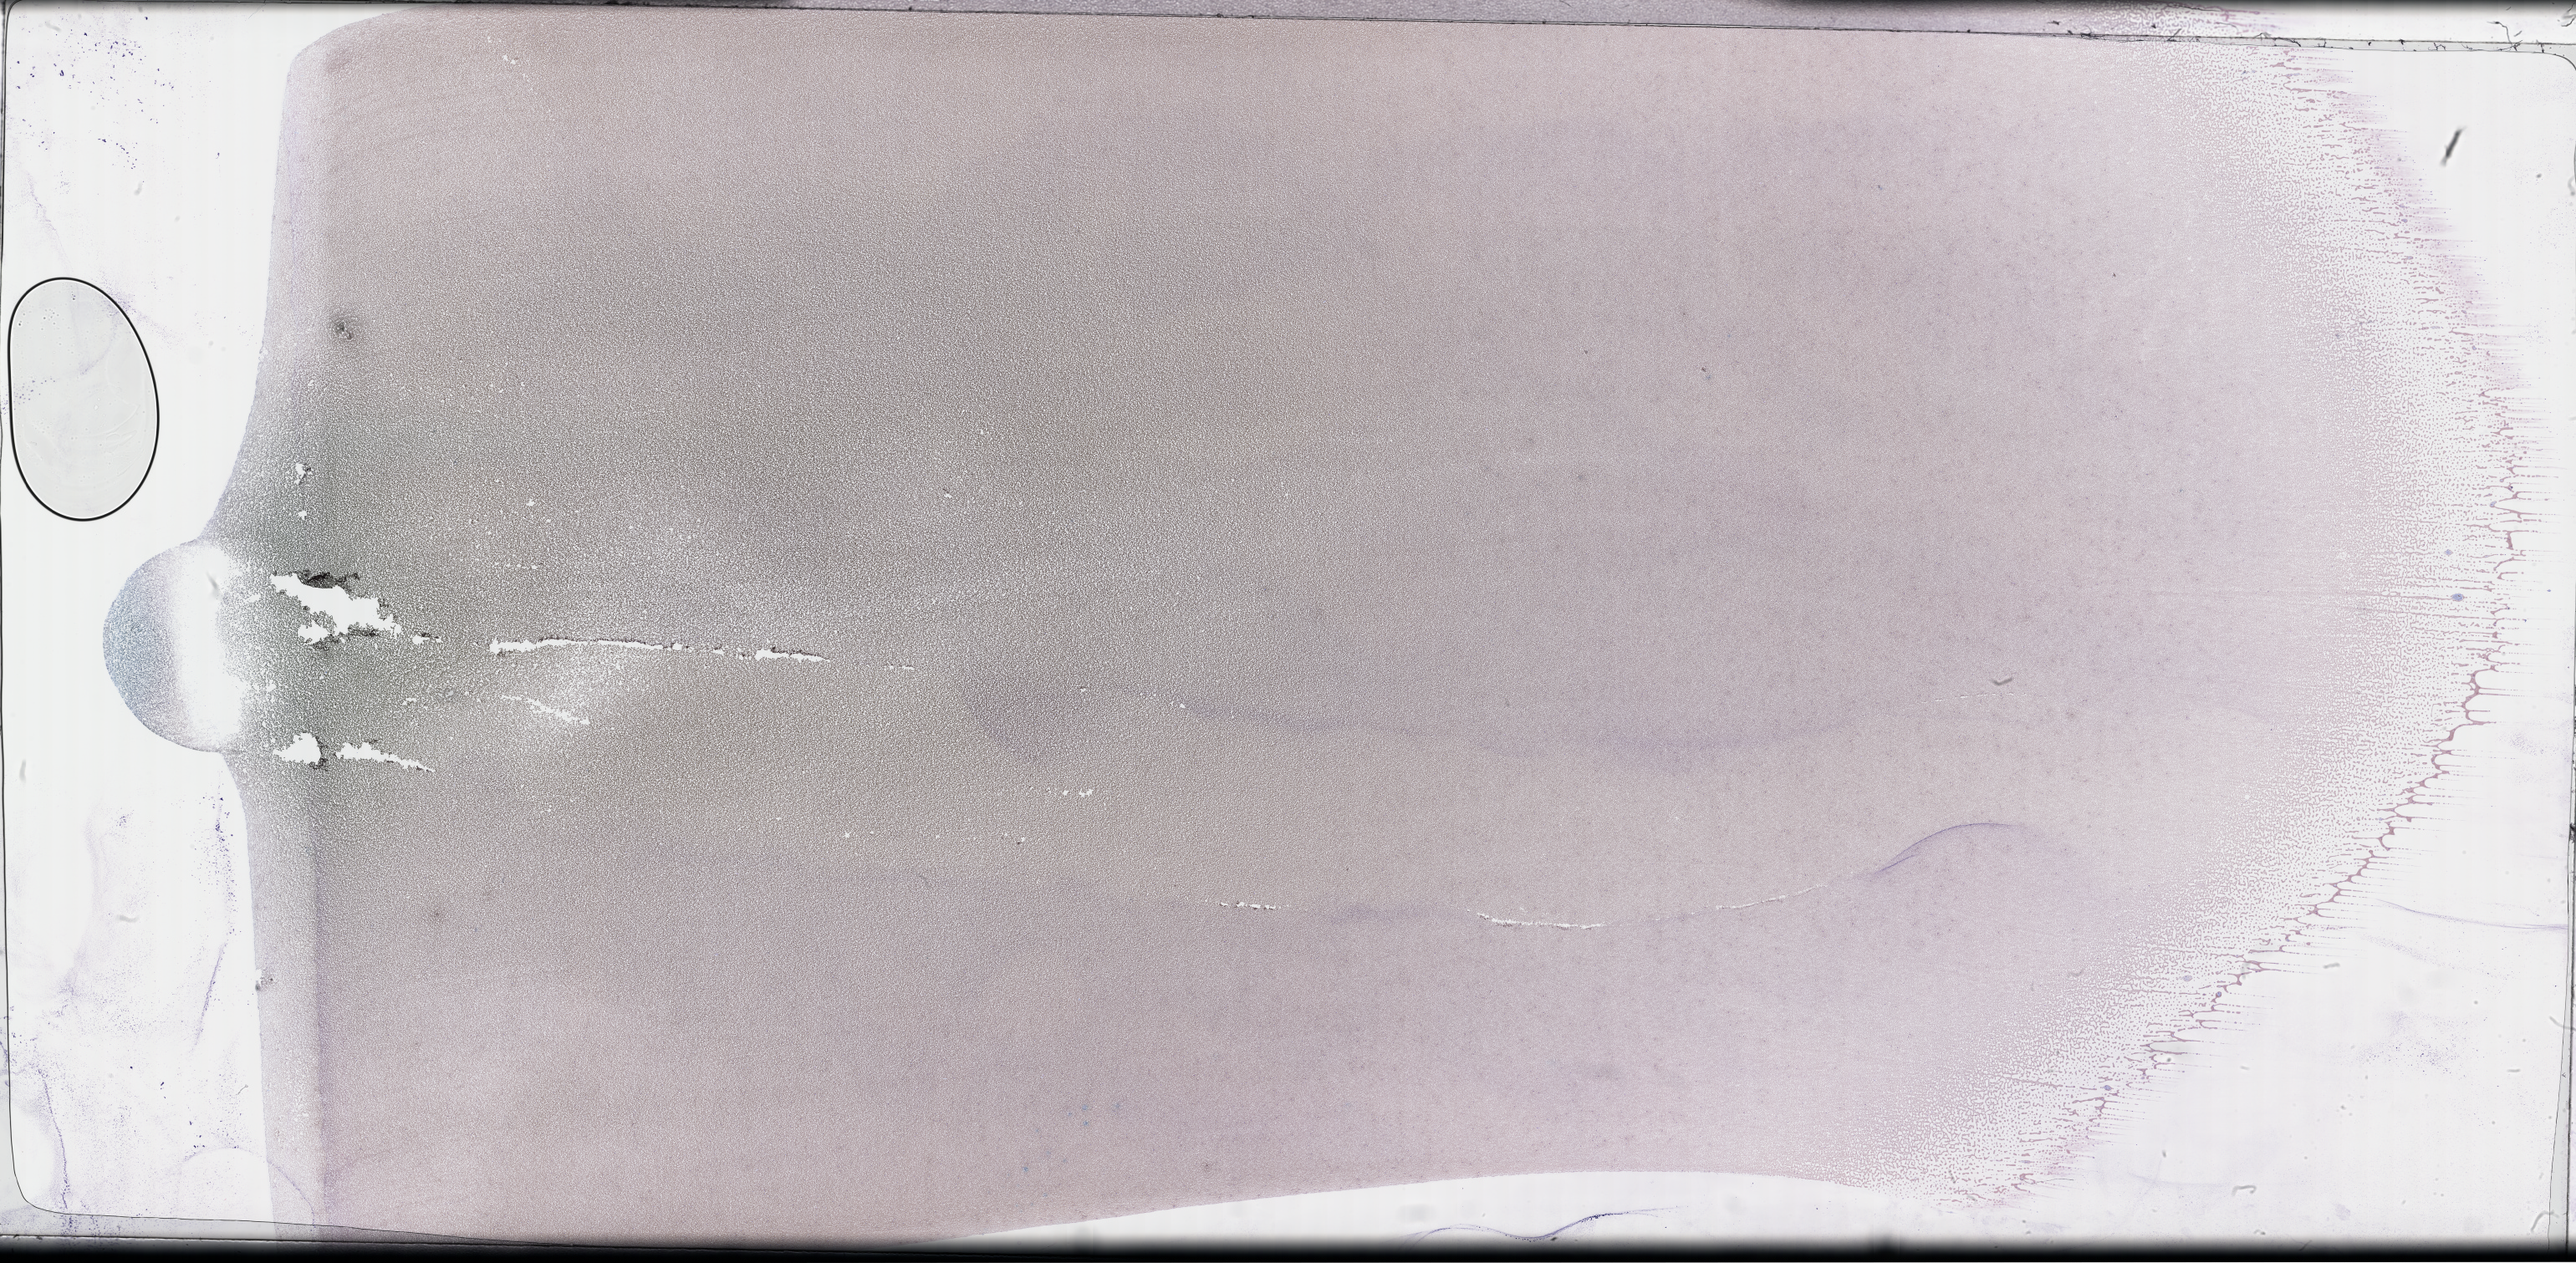
Wright–Giemsa-stained whole blood smear, whole-slide image — a low-resolution overview of the entire scanned area, about 49.8 x 24.4 mm; collected on treatment. Patient: female.
From a patient with: Plasma Cell Myeloma.